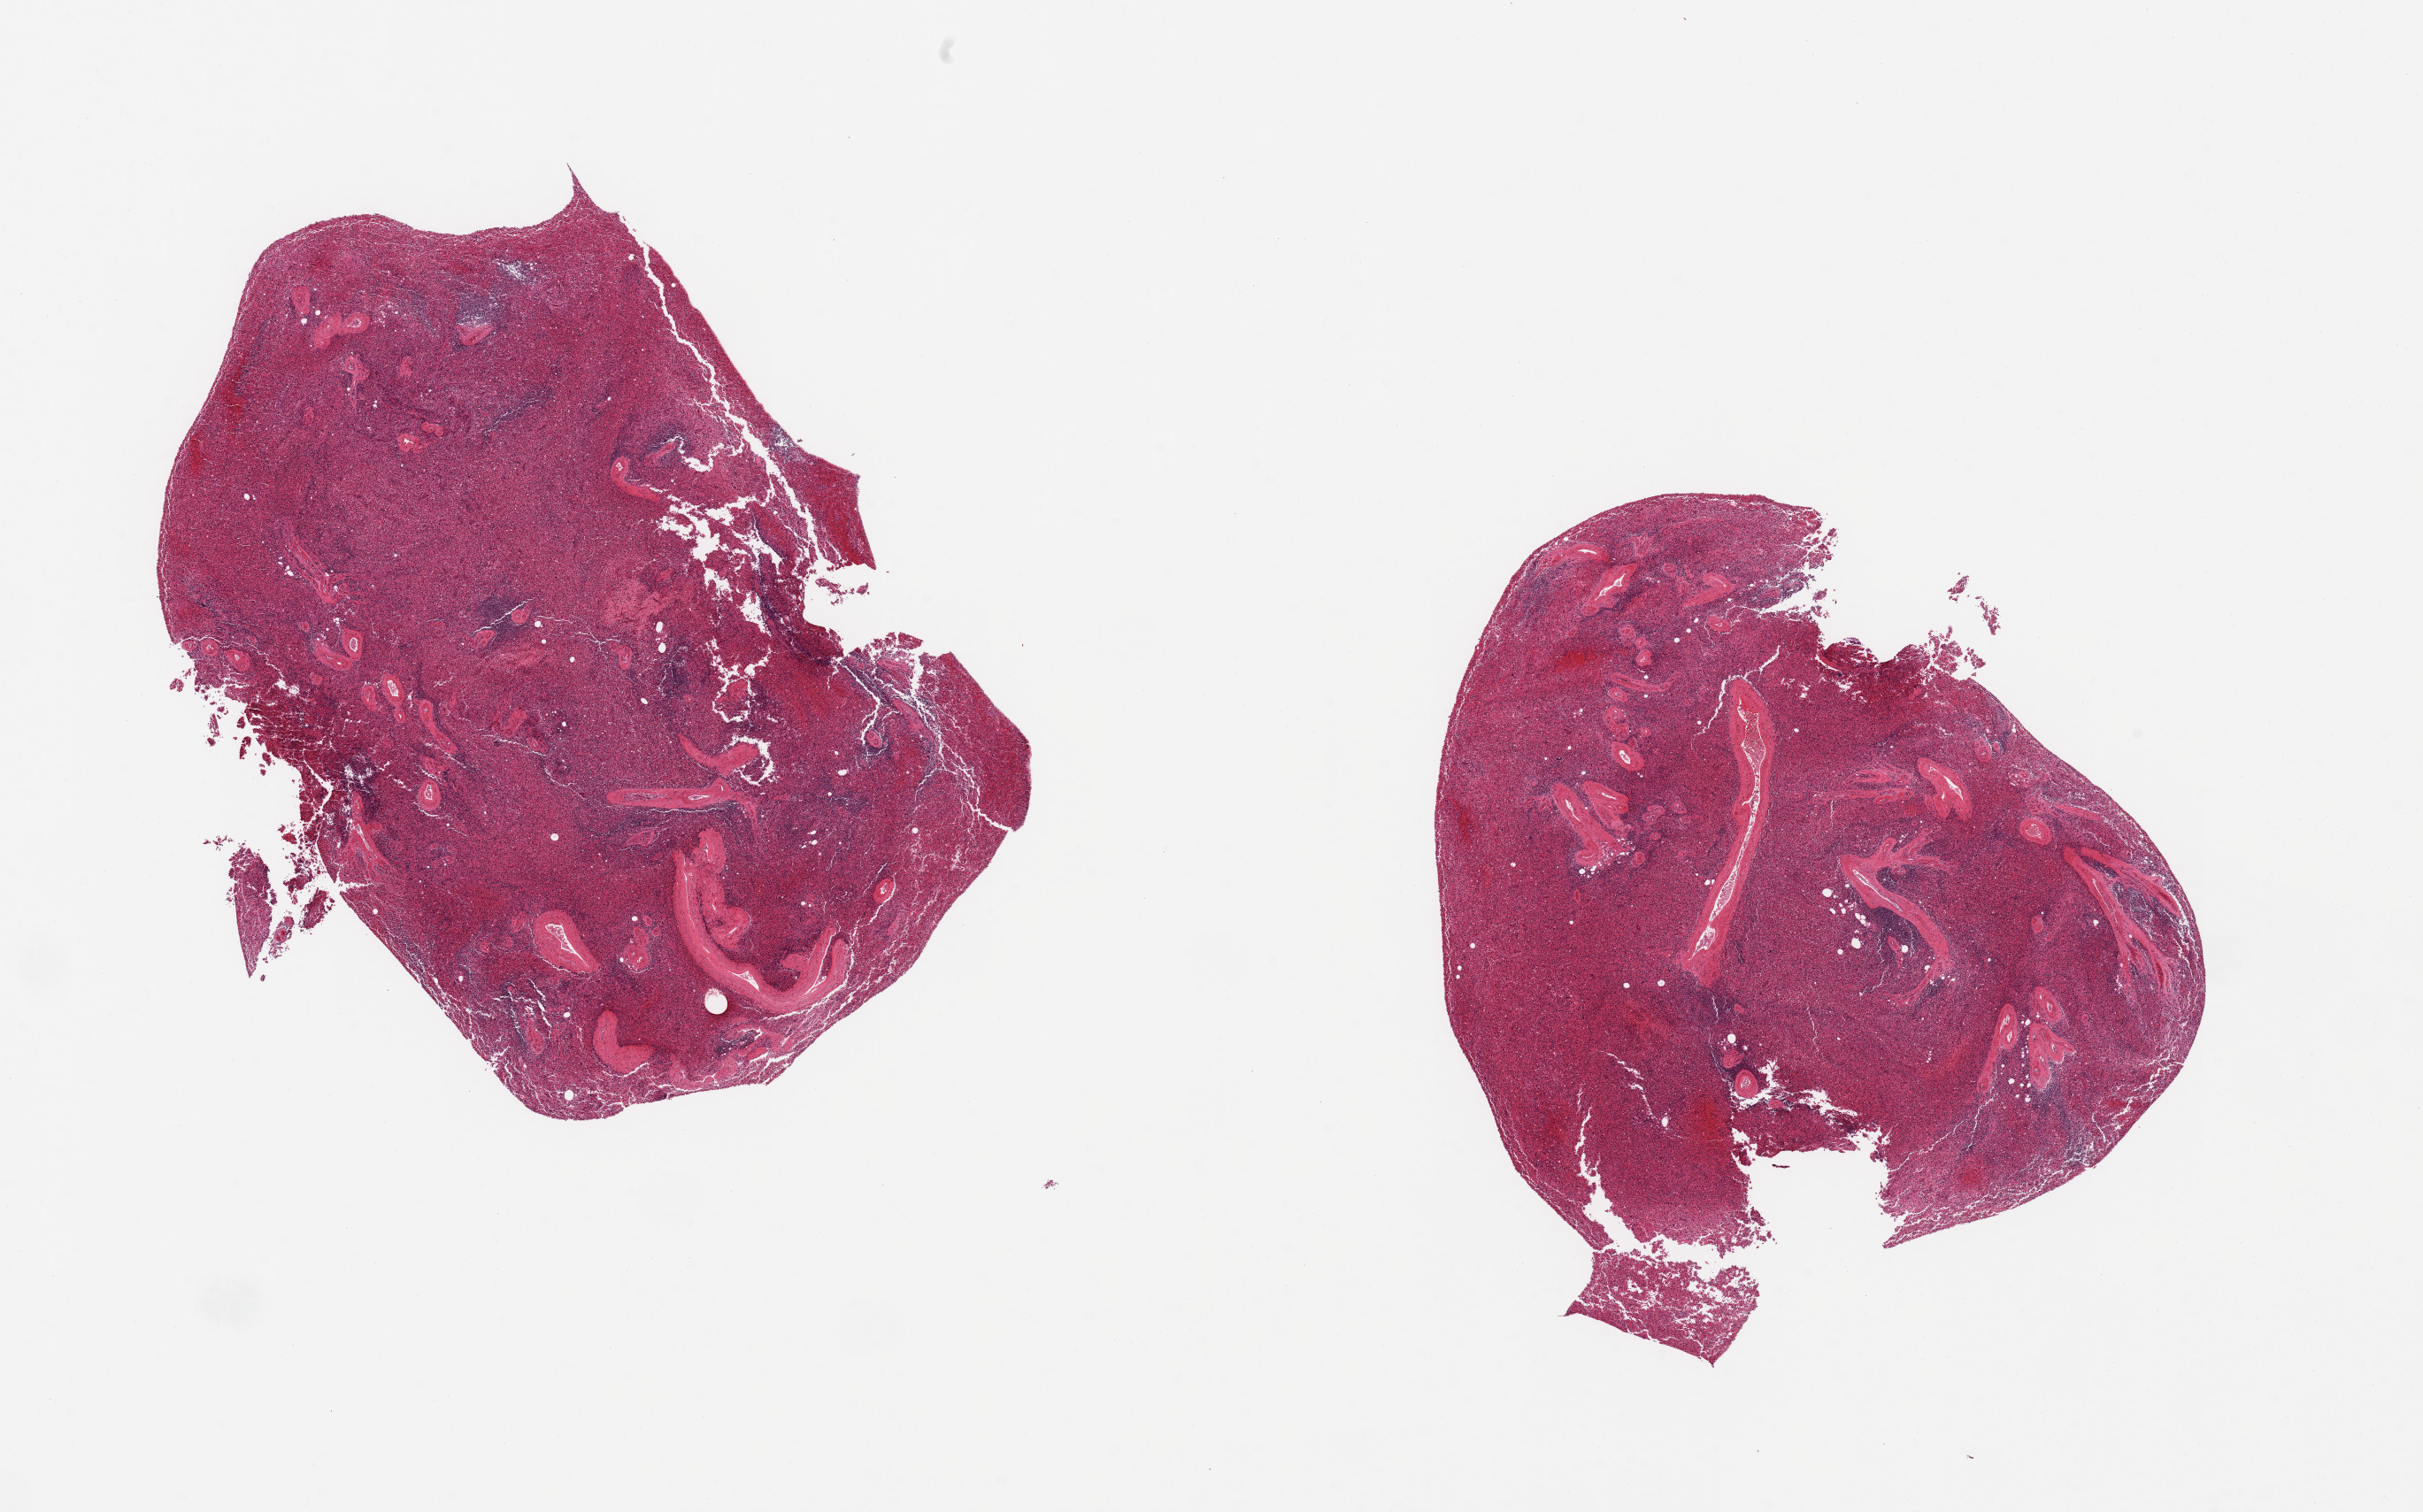
Haematoxylin and eosin whole-slide image, low-resolution overview of the scanned area, about 21.7 x 13.5 mm (slide scanned at 20x); PAXgene-fixed, paraffin-embedded tissue; sampled site (target tissue): spleen; donor tissue sample.
Review note (as recorded): 2 pieces; congestion.